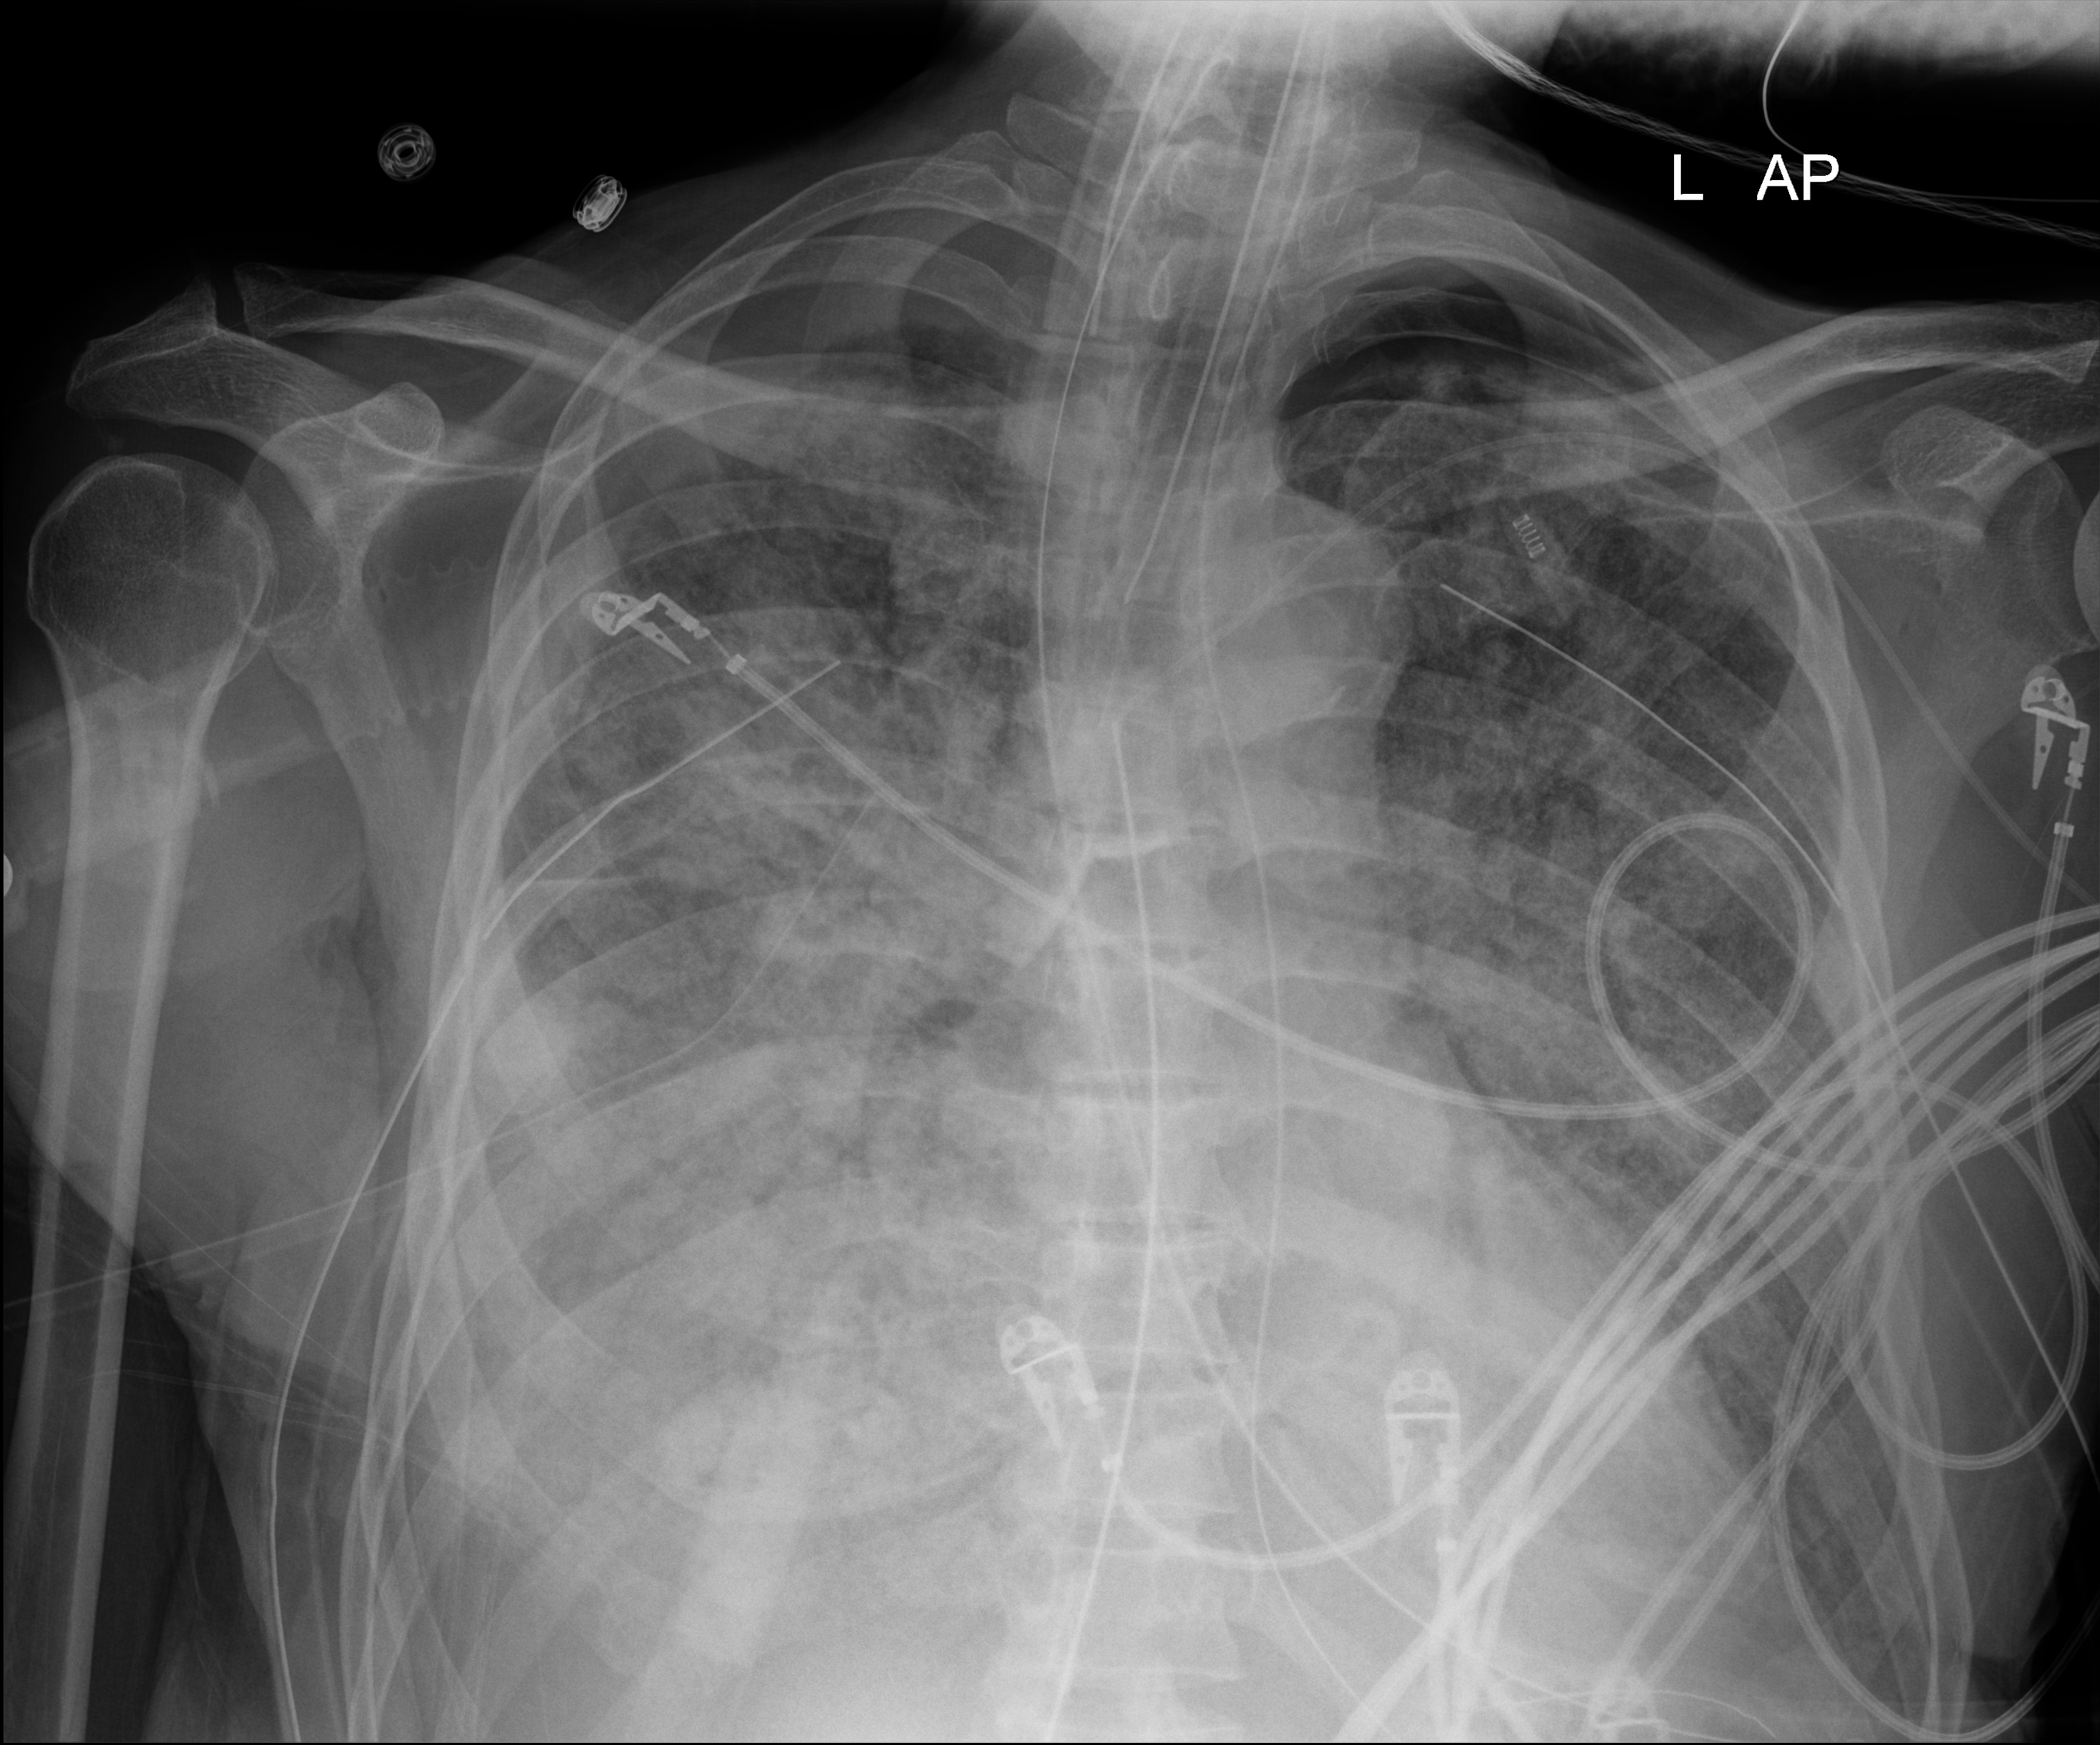
Chest X-ray (portable), anteroposterior (AP) projection. Patient hospitalised with COVID-19; male, aged 60–74 years.
From the hospital-stay record, not from the radiograph (when in the stay this image was taken is not recorded): mechanically ventilated during this hospital stay: yes; admitted to intensive care during this hospital stay: yes.